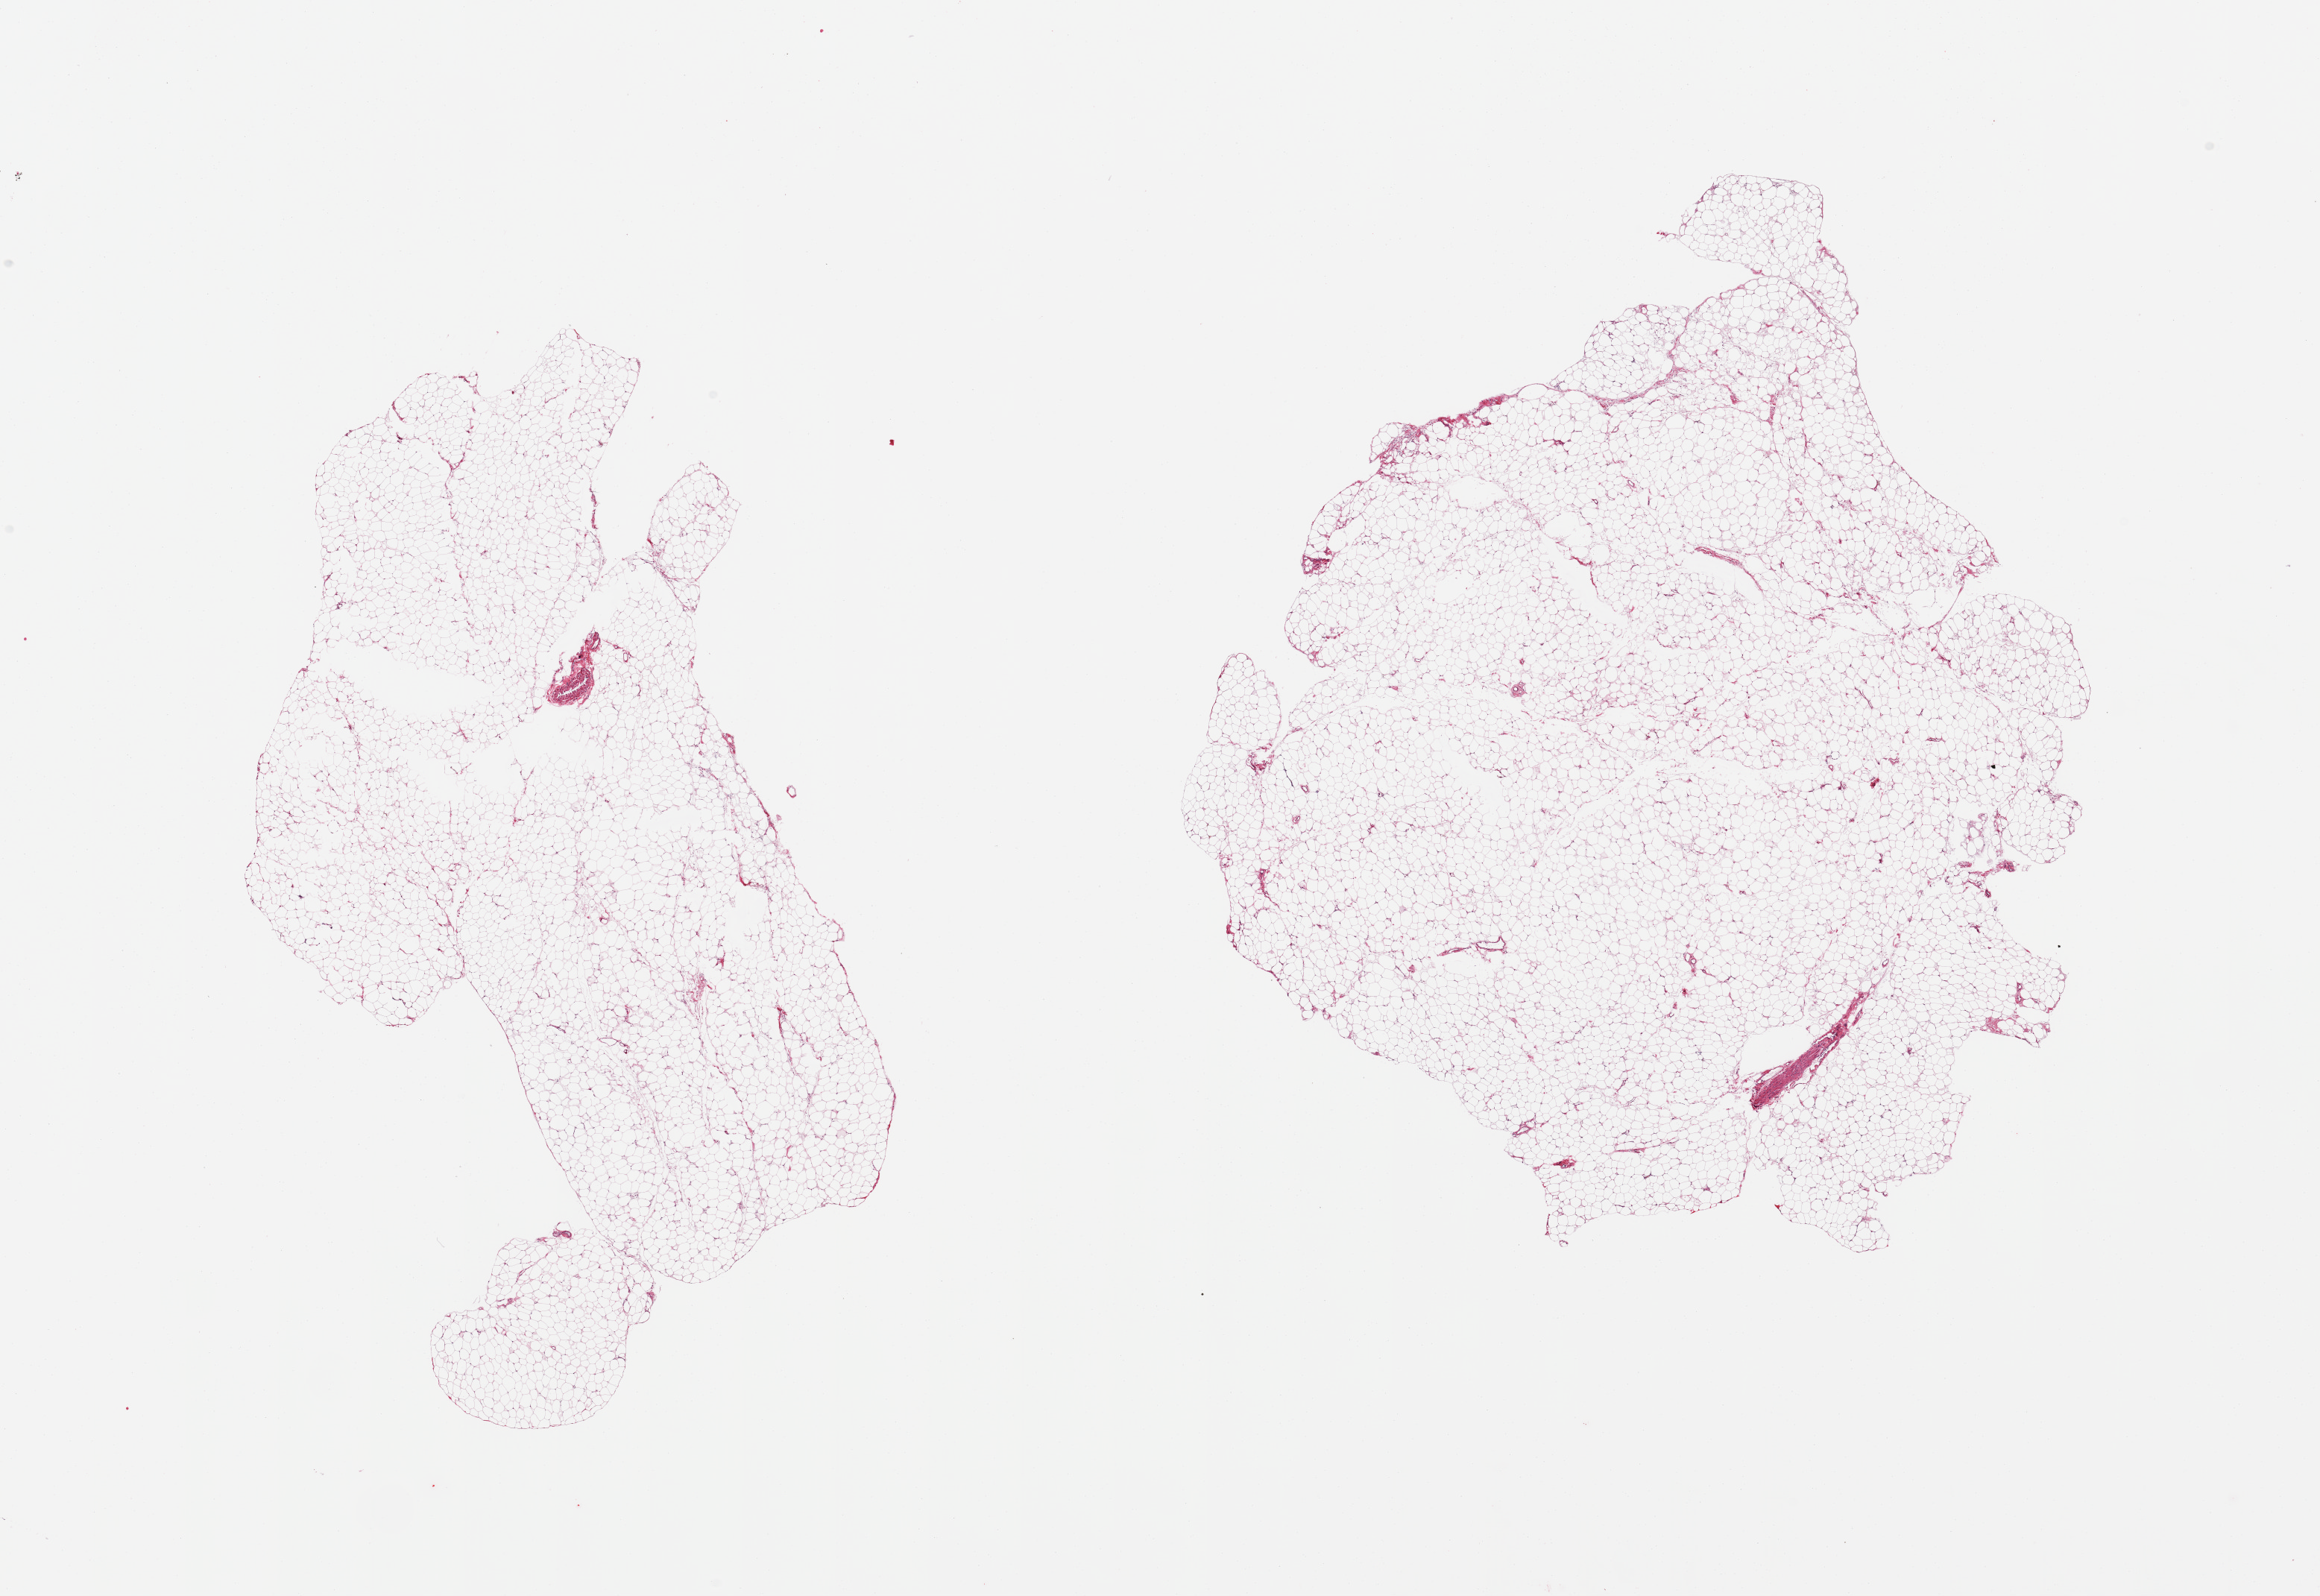
H&E whole-slide image, brightfield — low-resolution overview of the scanned area, about 24.6 x 16.9 mm, PAXgene-fixed, paraffin-embedded tissue, section of omentum (target tissue), tissue donor sample. Donor: male.
Reviewer comment on this tissue sample: 2 pieces, trace fascia.